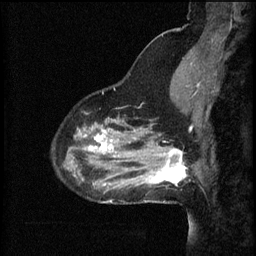
Breast MRI (dynamic contrast-enhanced), one sagittal slice; slice 17 of 60 in the series (ordered by position); 3 images stored at this slice position (order not interpretable as contrast timing); 1.5 T; TE 4.2 ms, TR 8.2 ms; 2 mm slice thickness; 256 × 256 image matrix, field of view 200 × 200 mm. Female patient, age 37 years.
Annotated regions visible in this slice (semi-automatic segmentation, software-assisted and operator-edited):
- analysis volume of interest (the breast-tissue region the enhancement analysis was run in; not a lesion): bounding box (x1, y1, x2, y2) in pixels: (148, 140, 195, 187)
- tumour enhancement mask (voxels above the 70 % enhancement threshold inside the analysis volume of interest): (148, 148, 189, 185)